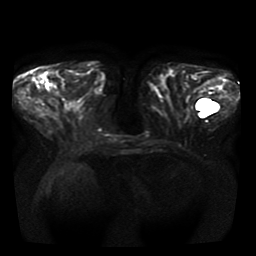
Breast MRI, one axial slice. Position 13 of 41 along the scan axis. Diffusion-weighted series; image 2 of 4 stored at this slice position (different b-values; order by instance number). 1.5 T. 5 mm slice thickness. 256 × 256 image matrix, field of view 350 × 350 mm. Female patient.
Annotated regions visible in this slice (expert manual segmentation):
- tumour on diffusion-weighted imaging: box from (x=30, y=70) to (x=41, y=85) px